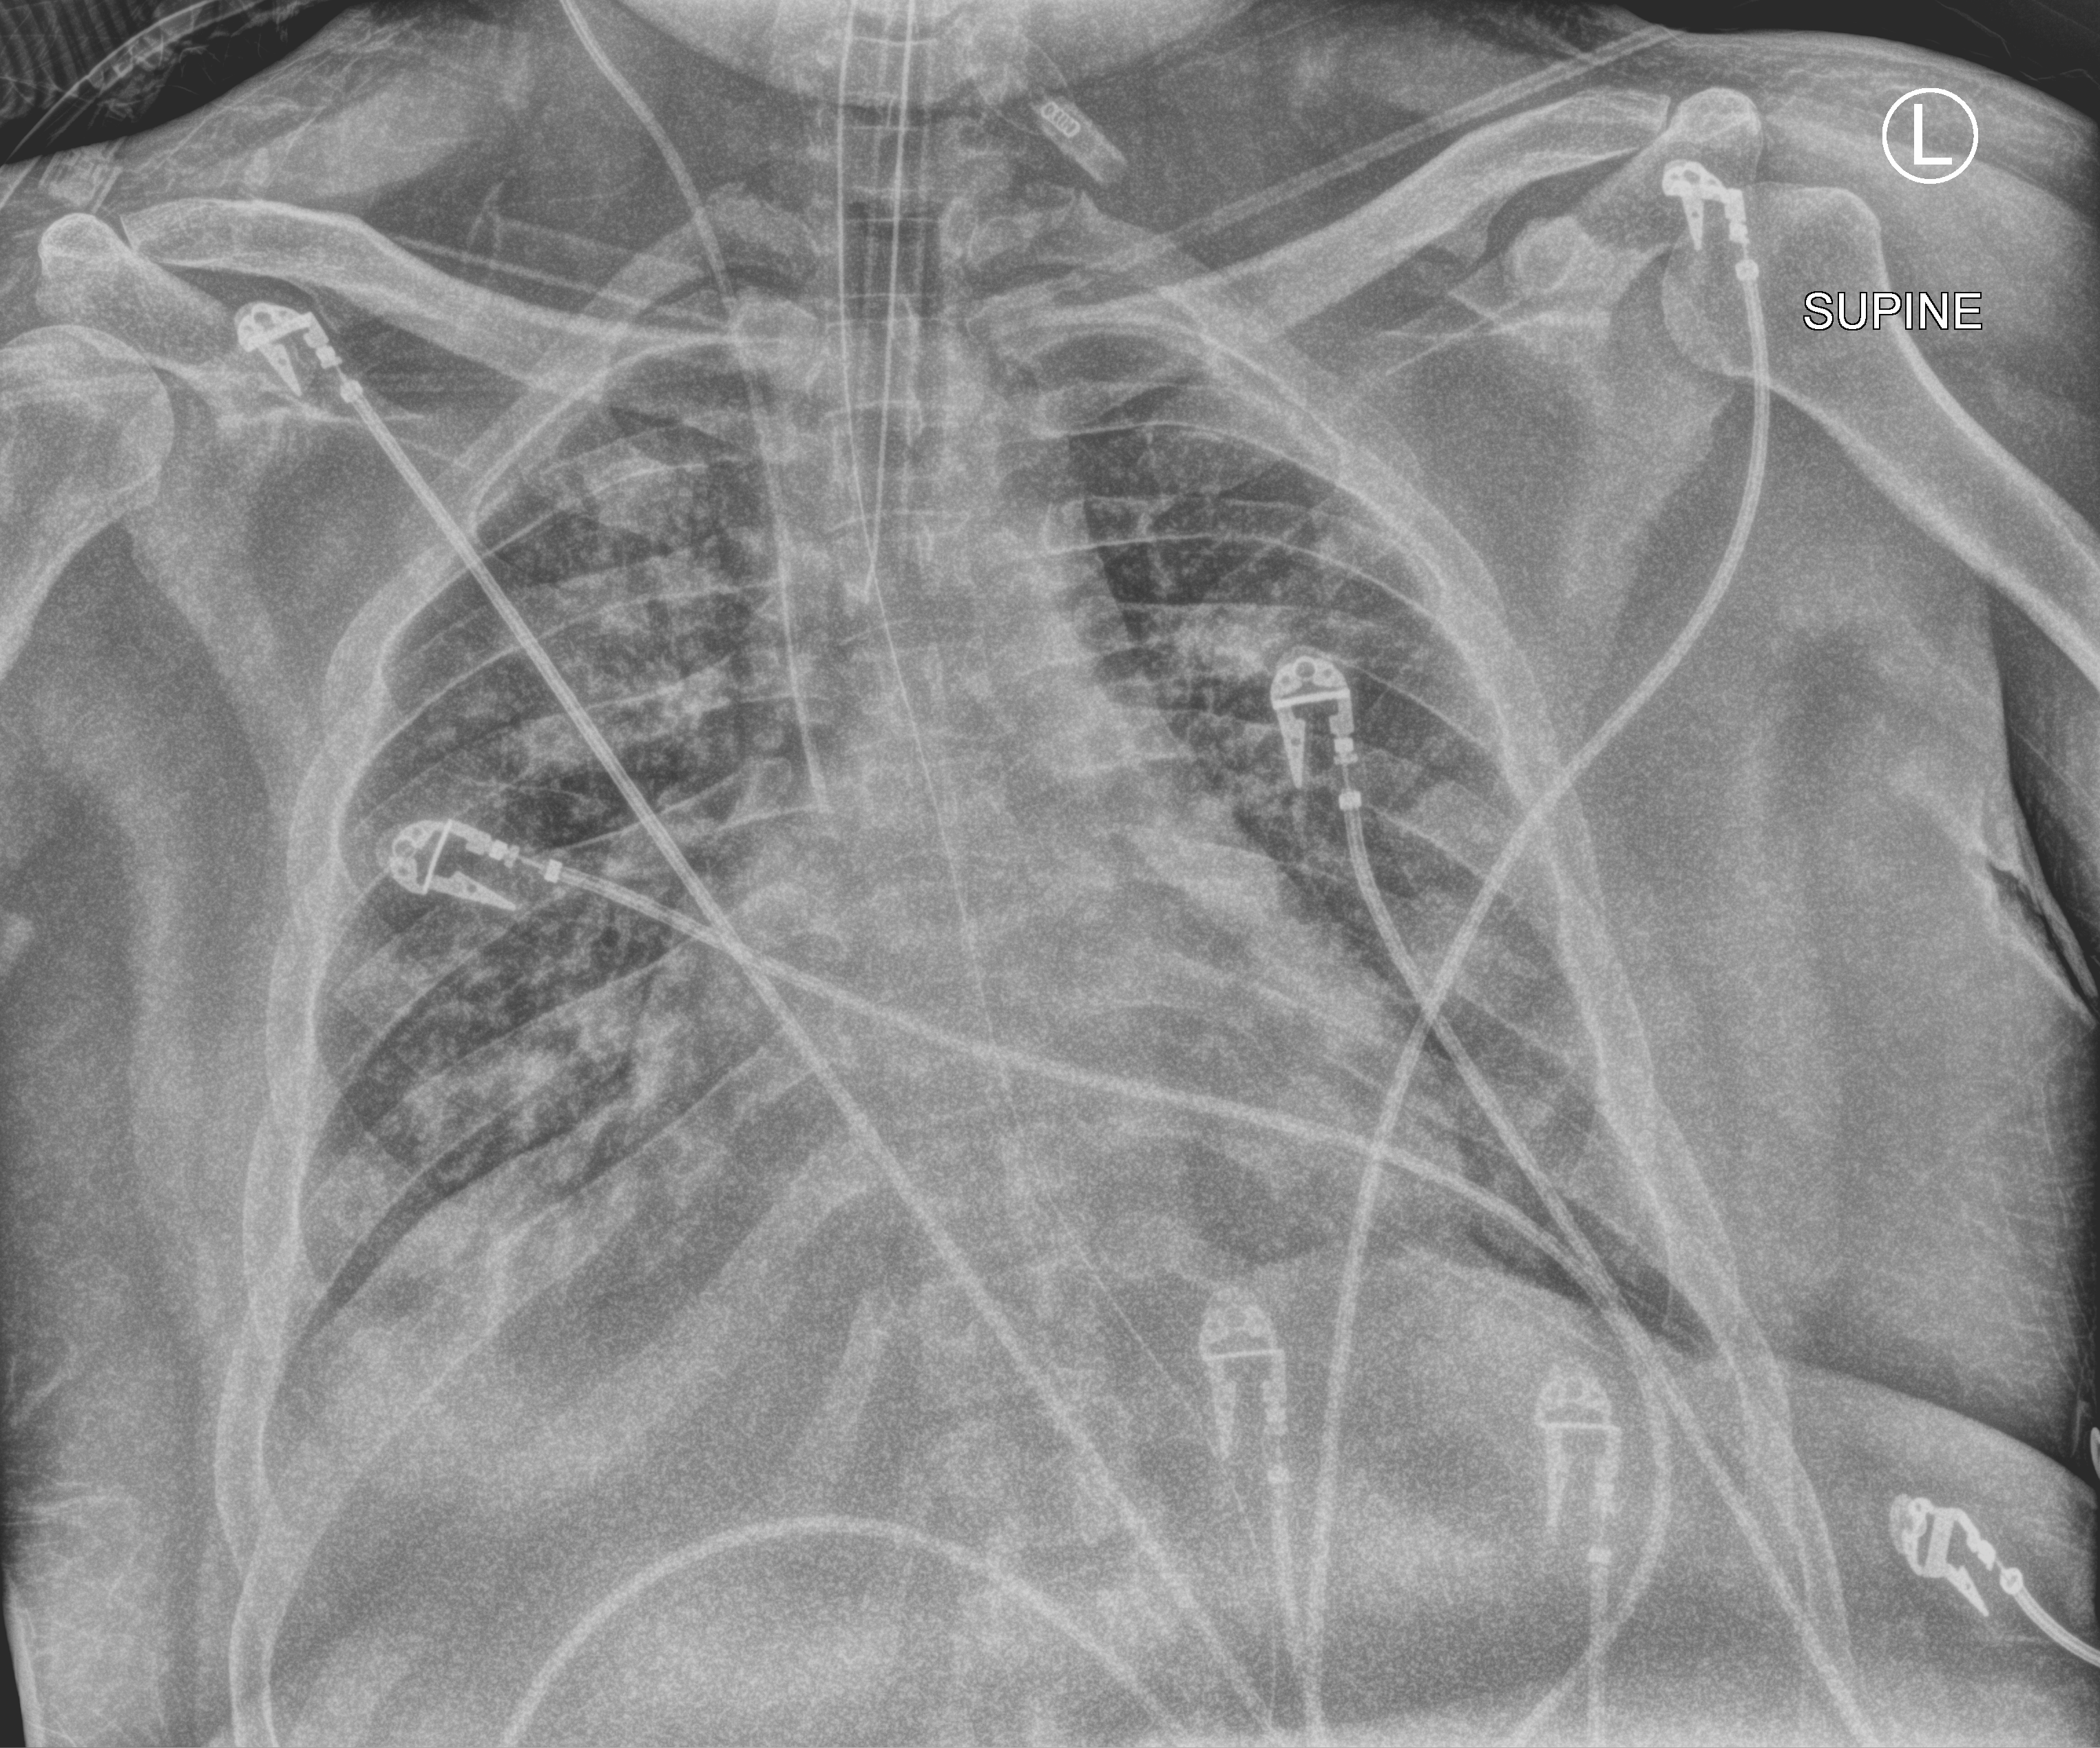
Chest X-ray (portable); anteroposterior (AP) projection. Patient hospitalised with COVID-19, aged 18–59 years.
From the hospital-stay record, not from the radiograph (when in the stay this image was taken is not recorded):
- admitted to intensive care during this hospital stay: yes